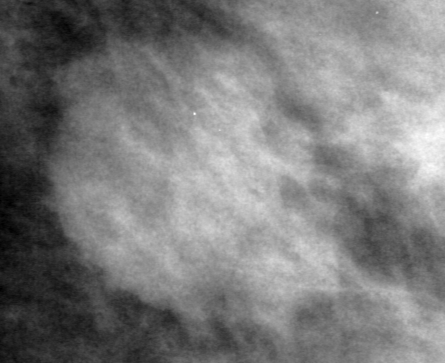
Crop from a digitized film mammogram around one marked abnormality, left breast, MLO view.
Finding: mass, shape lobulated, margins microlobulated; BI-RADS assessment category 3; subtlety rating 5 on a 1 (subtle) to 5 (obvious) scale; pathology (as recorded): benign.